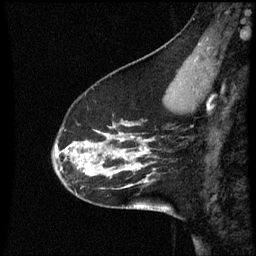
Breast MRI (dynamic contrast-enhanced), one sagittal slice; slice 16 of 60 in the series (ordered by position); dynamic contrast-enhanced series, image 2 of 3 at this slice position (ordered by acquisition); 1.5 T; TE 4.2 ms, TR 8.9 ms; 256 × 256 image matrix, field of view 200 × 200 mm. Patient: female, 45 years. Case-level facts recorded for this patient, not image findings: setting: breast cancer imaged before/during neoadjuvant chemotherapy; receptor status: HR-positive, HER2-negative.
Outlined on this slice (semi-automatically segmented with operator editing):
- analysis volume of interest (the breast-tissue region the enhancement analysis was run in; not a lesion): bounding box <52,94,171,205> (left, top, right, bottom; pixels)
- tumour enhancement mask (voxels above the 70 % enhancement threshold inside the analysis volume of interest): <56,140,149,175>